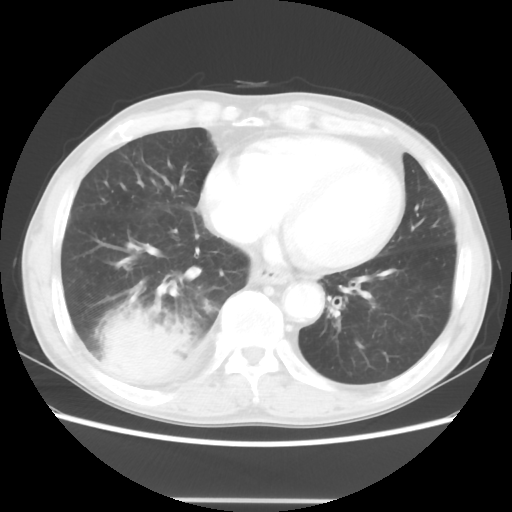
Chest CT, one axial slice. Position 13 of 48 along the scan axis. Reconstruction kernel STANDARD. 100 kVp. Lung window (W 1500 / L -600 HU). 512 × 512 image matrix. Patient: male, 66 years. Case-level facts recorded for this patient, not image findings: clinical TNM (as recorded): T4 N1 M1; histopathological grade: G3.
Outlined on this slice (rectangle marked by the reading radiologist):
- lung tumour (recorded histology: small cell carcinoma): bounding box <98,299,198,386> (left, top, right, bottom; pixels)